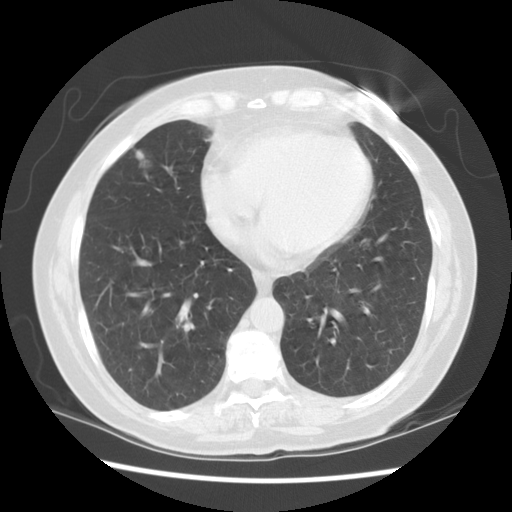
Low-dose screening chest CT, one axial slice. Position 45 of 115 along the scan axis. Lung window (W 1500 / L -600 HU). 512 × 512 image matrix, field of view 340 × 340 mm.
Structures marked on this image (expert manual segmentation):
- lesion 1 (tumor, middle lobe of right lung): bounding box [x1, y1, x2, y2] px = [136, 150, 144, 160]